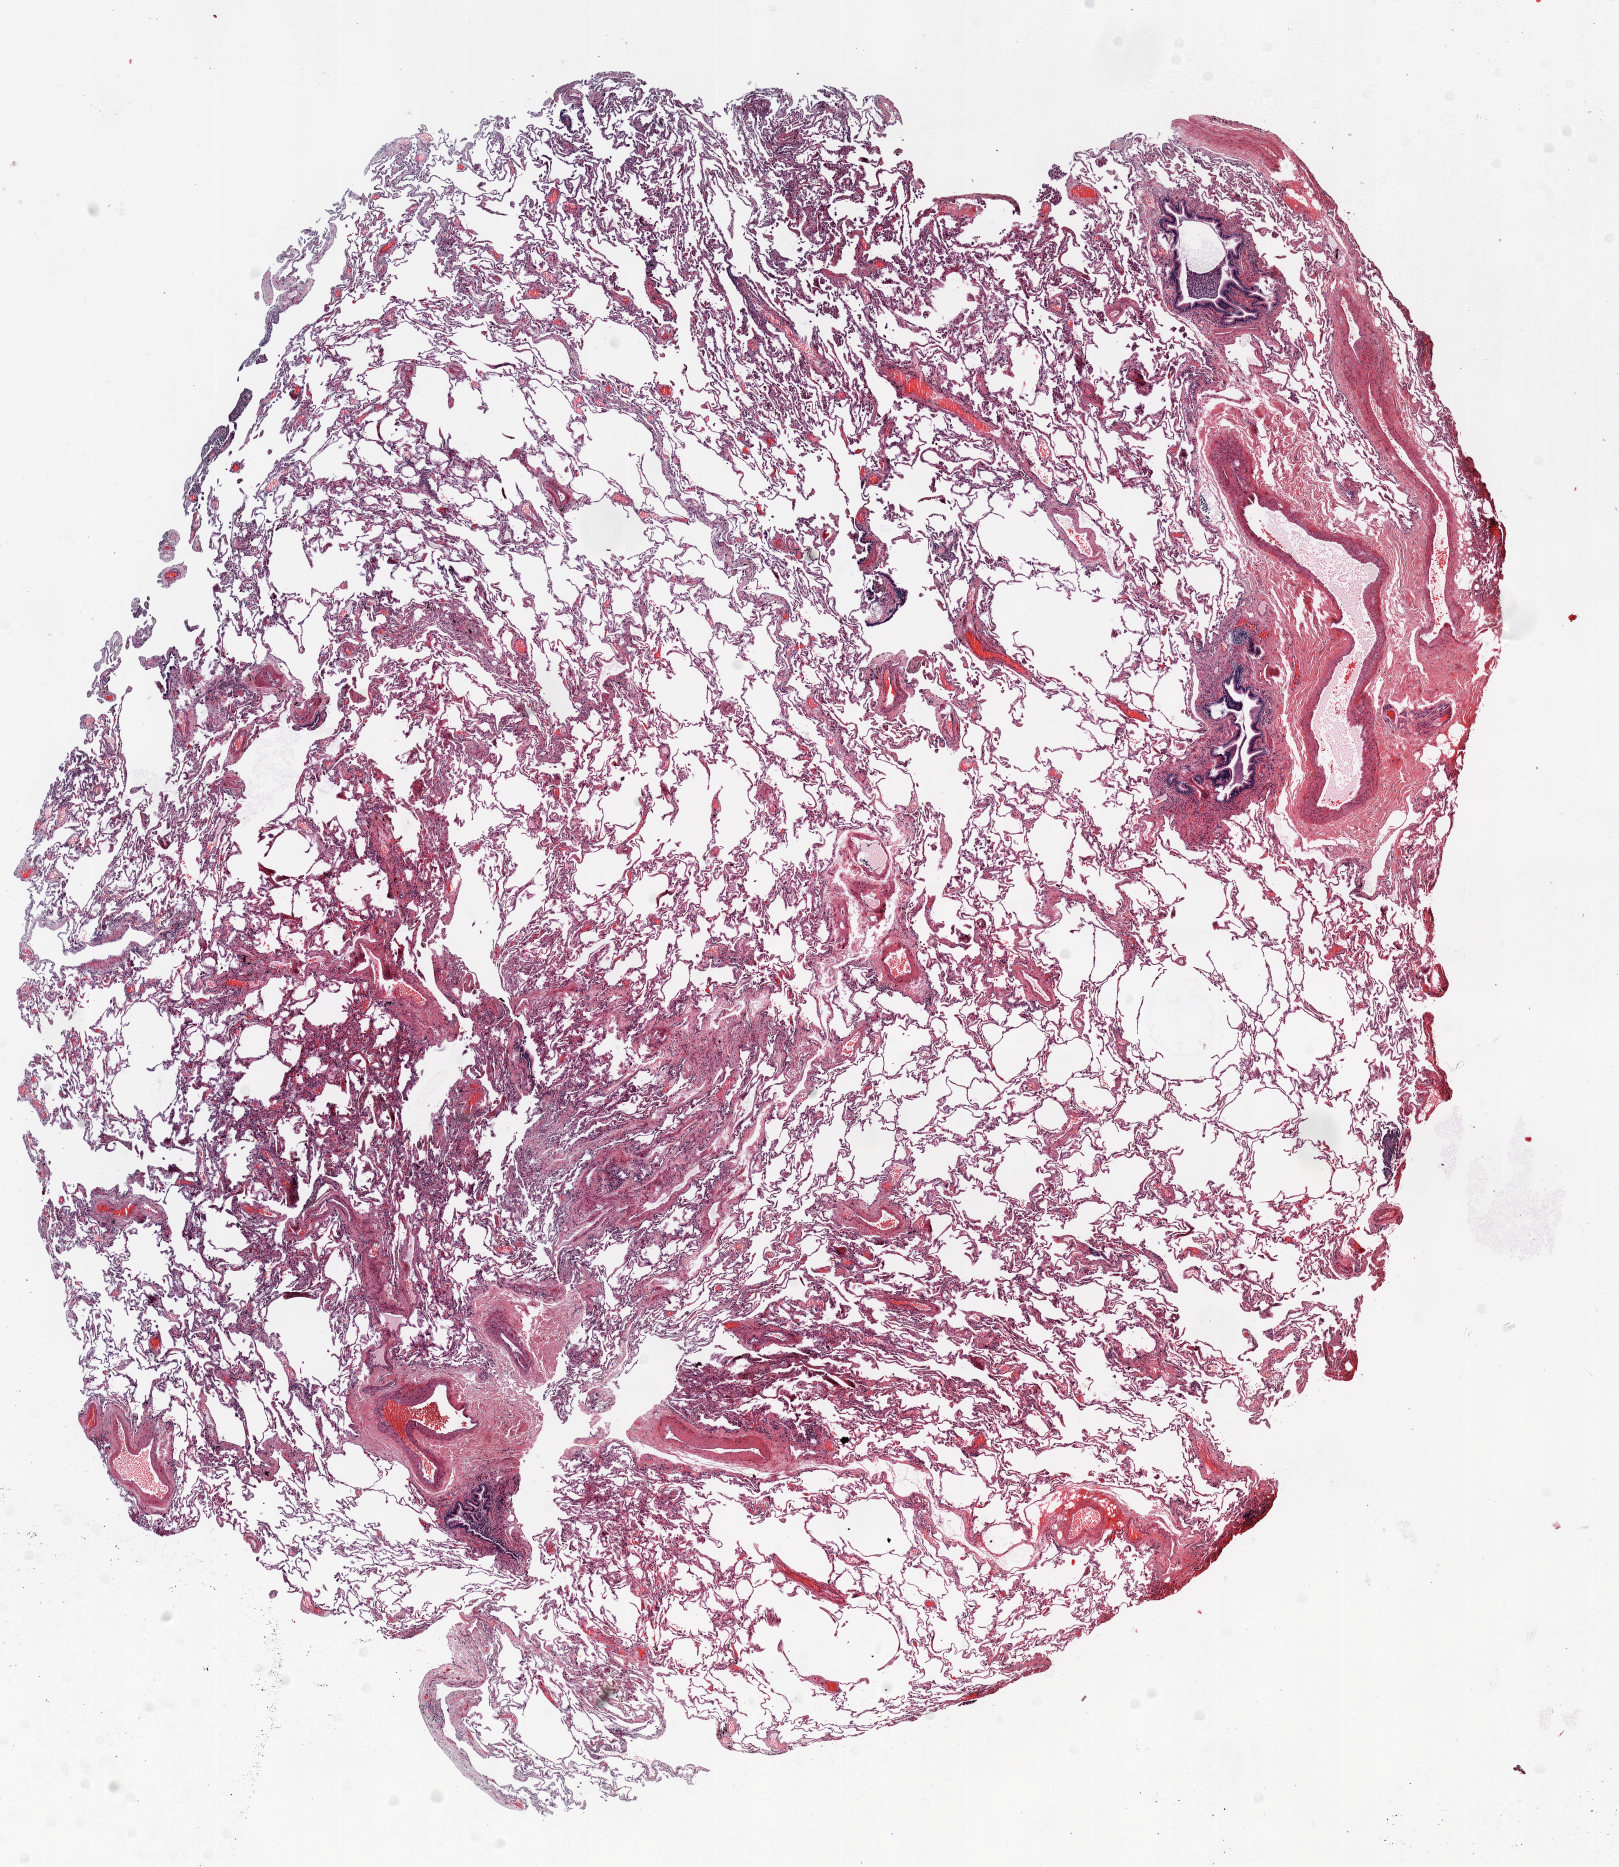
H&E whole-slide image, whole scanned area (about 13.0 x 15.0 mm) shown as a low-resolution overview, FFPE section, lung. Male, age 61 at enrolment. Current smoker at enrolment. Grade: poorly differentiated (G3).
* stage (AJCC 6th edition): IIIA
* participant's lung-cancer diagnosis: Adenocarcinoma, NOS (ICD-O-3 8140/3)
* tumour size (pathology): 30 mm
* primary tumour location (clinical record): left upper lobe